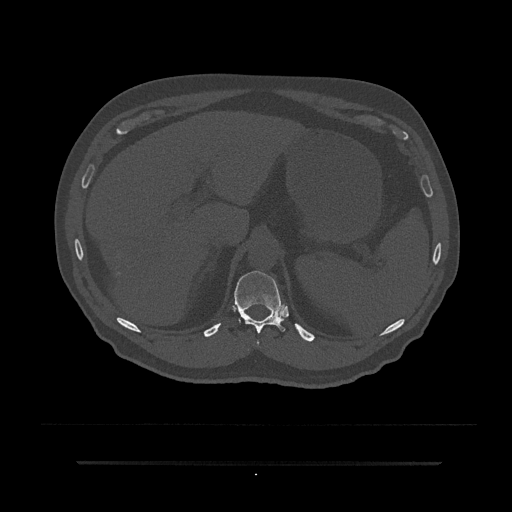
CT including the spine, one axial slice. Position 267 of 797 along the scan axis. Reconstruction kernel Br40s/3. 120 kVp. Bone window (W 1800 / L 400 HU). 0.5 mm slice thickness. 512 × 512 image matrix, field of view 464 × 464 mm. Male patient, age 59 years. From the clinical record (not read from this slice): primary cancer: bile ducts.
Annotated regions visible in this slice (semi-automatically segmented with operator editing):
- T11 vertebra: box from (x=233, y=271) to (x=285, y=343) px